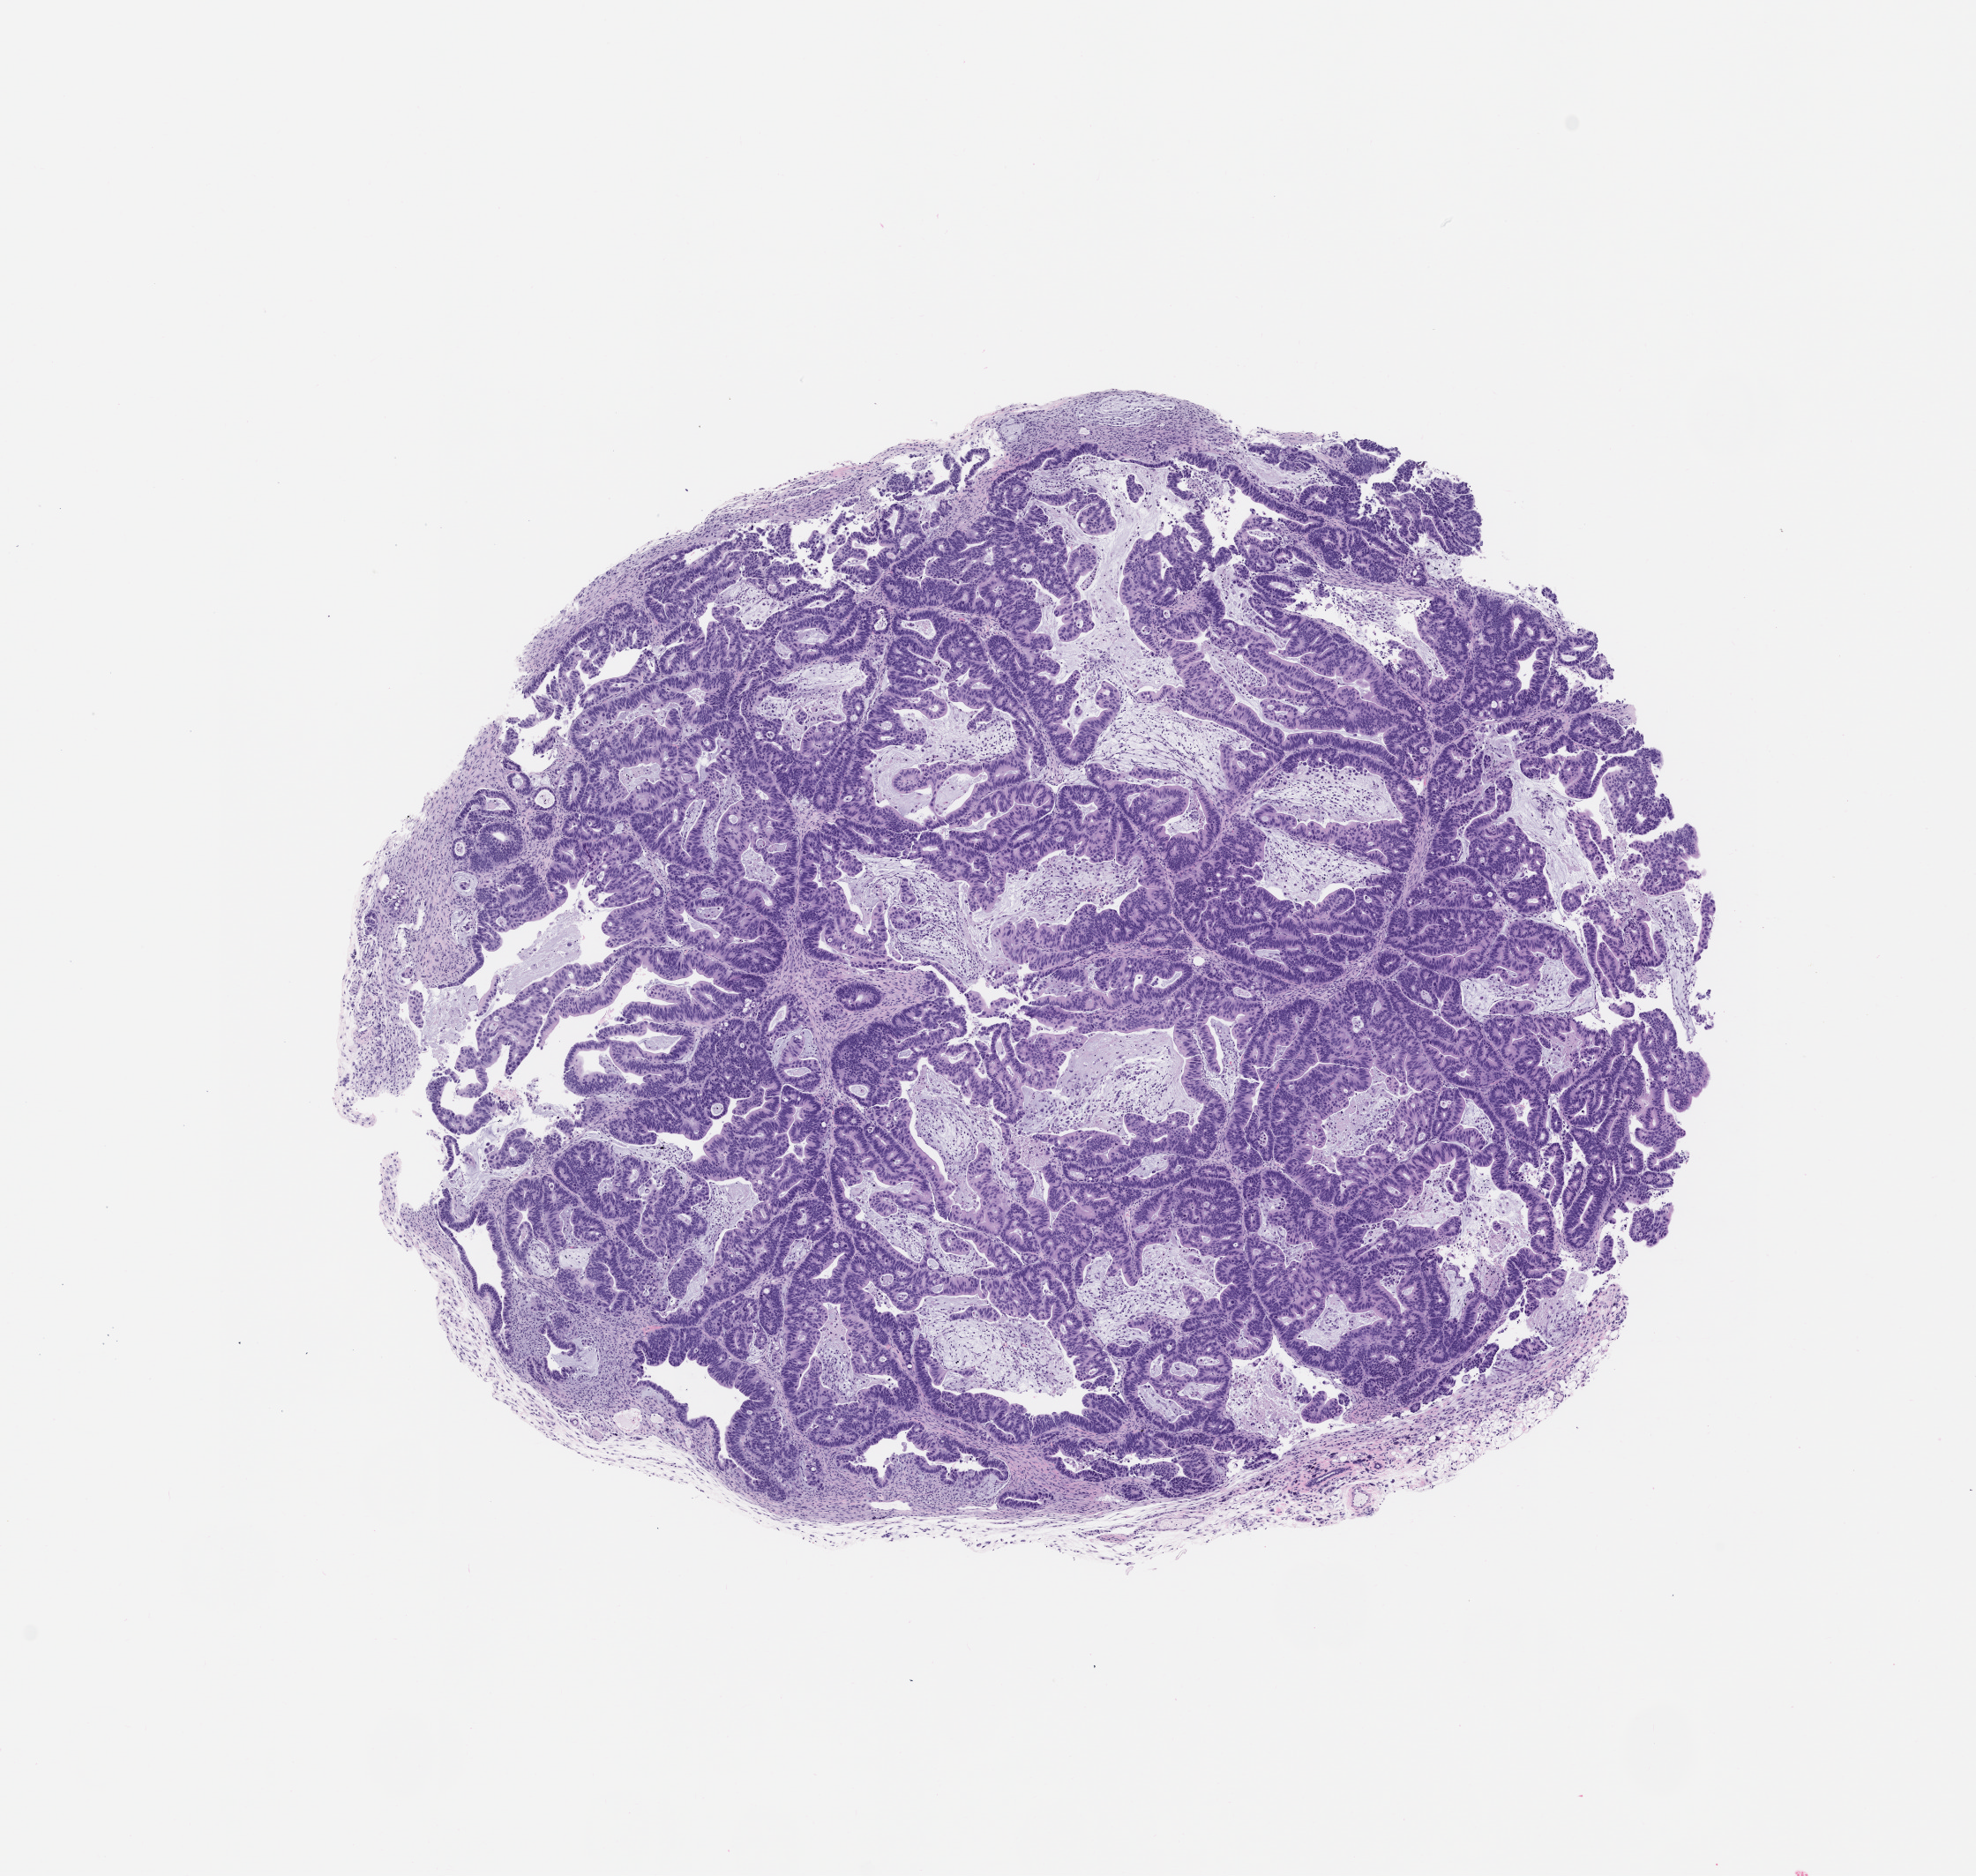
Haematoxylin and eosin whole-slide image of a patient-derived xenograft (PDX) tumor grown in a mouse, passage 1, shown as a low-resolution overview of the whole scanned area (about 9.0 x 8.5 mm), FFPE section, tumor site category: colon.
Originating patient diagnosis: Colon Adenocarcinoma.